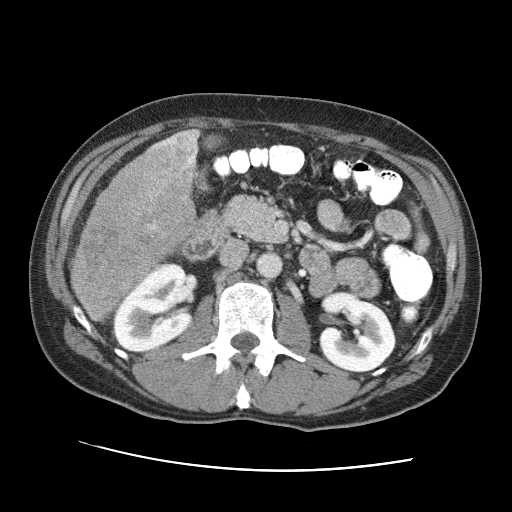
Contrast-enhanced abdominal CT (liver protocol), one axial slice; position 26 of 95 along the scan axis; one of 2 acquisitions stored at this slice position; soft-tissue window (W 400 / L 40 HU); 2.5 mm slice thickness; 512 × 512 image matrix, field of view 360 × 360 mm. From the clinical record (not read from this slice): diagnosis: hepatocellular carcinoma (patient treated with transarterial chemoembolisation; whether this scan precedes or follows treatment is not stated here); TNM stage (as recorded): Stage-IVA; Child-Pugh class: A; tumour differentiation: moderately differentiated; tumour nodularity: multinodular.
Structures marked on this image (semi-automatically segmented with operator editing):
- liver parenchyma outside the tumour (the mass and vessels are separate outlines, so this box may not span the whole liver): bounding box (x1, y1, x2, y2) in pixels: (72, 130, 198, 263)
- mass: (70, 129, 196, 324)